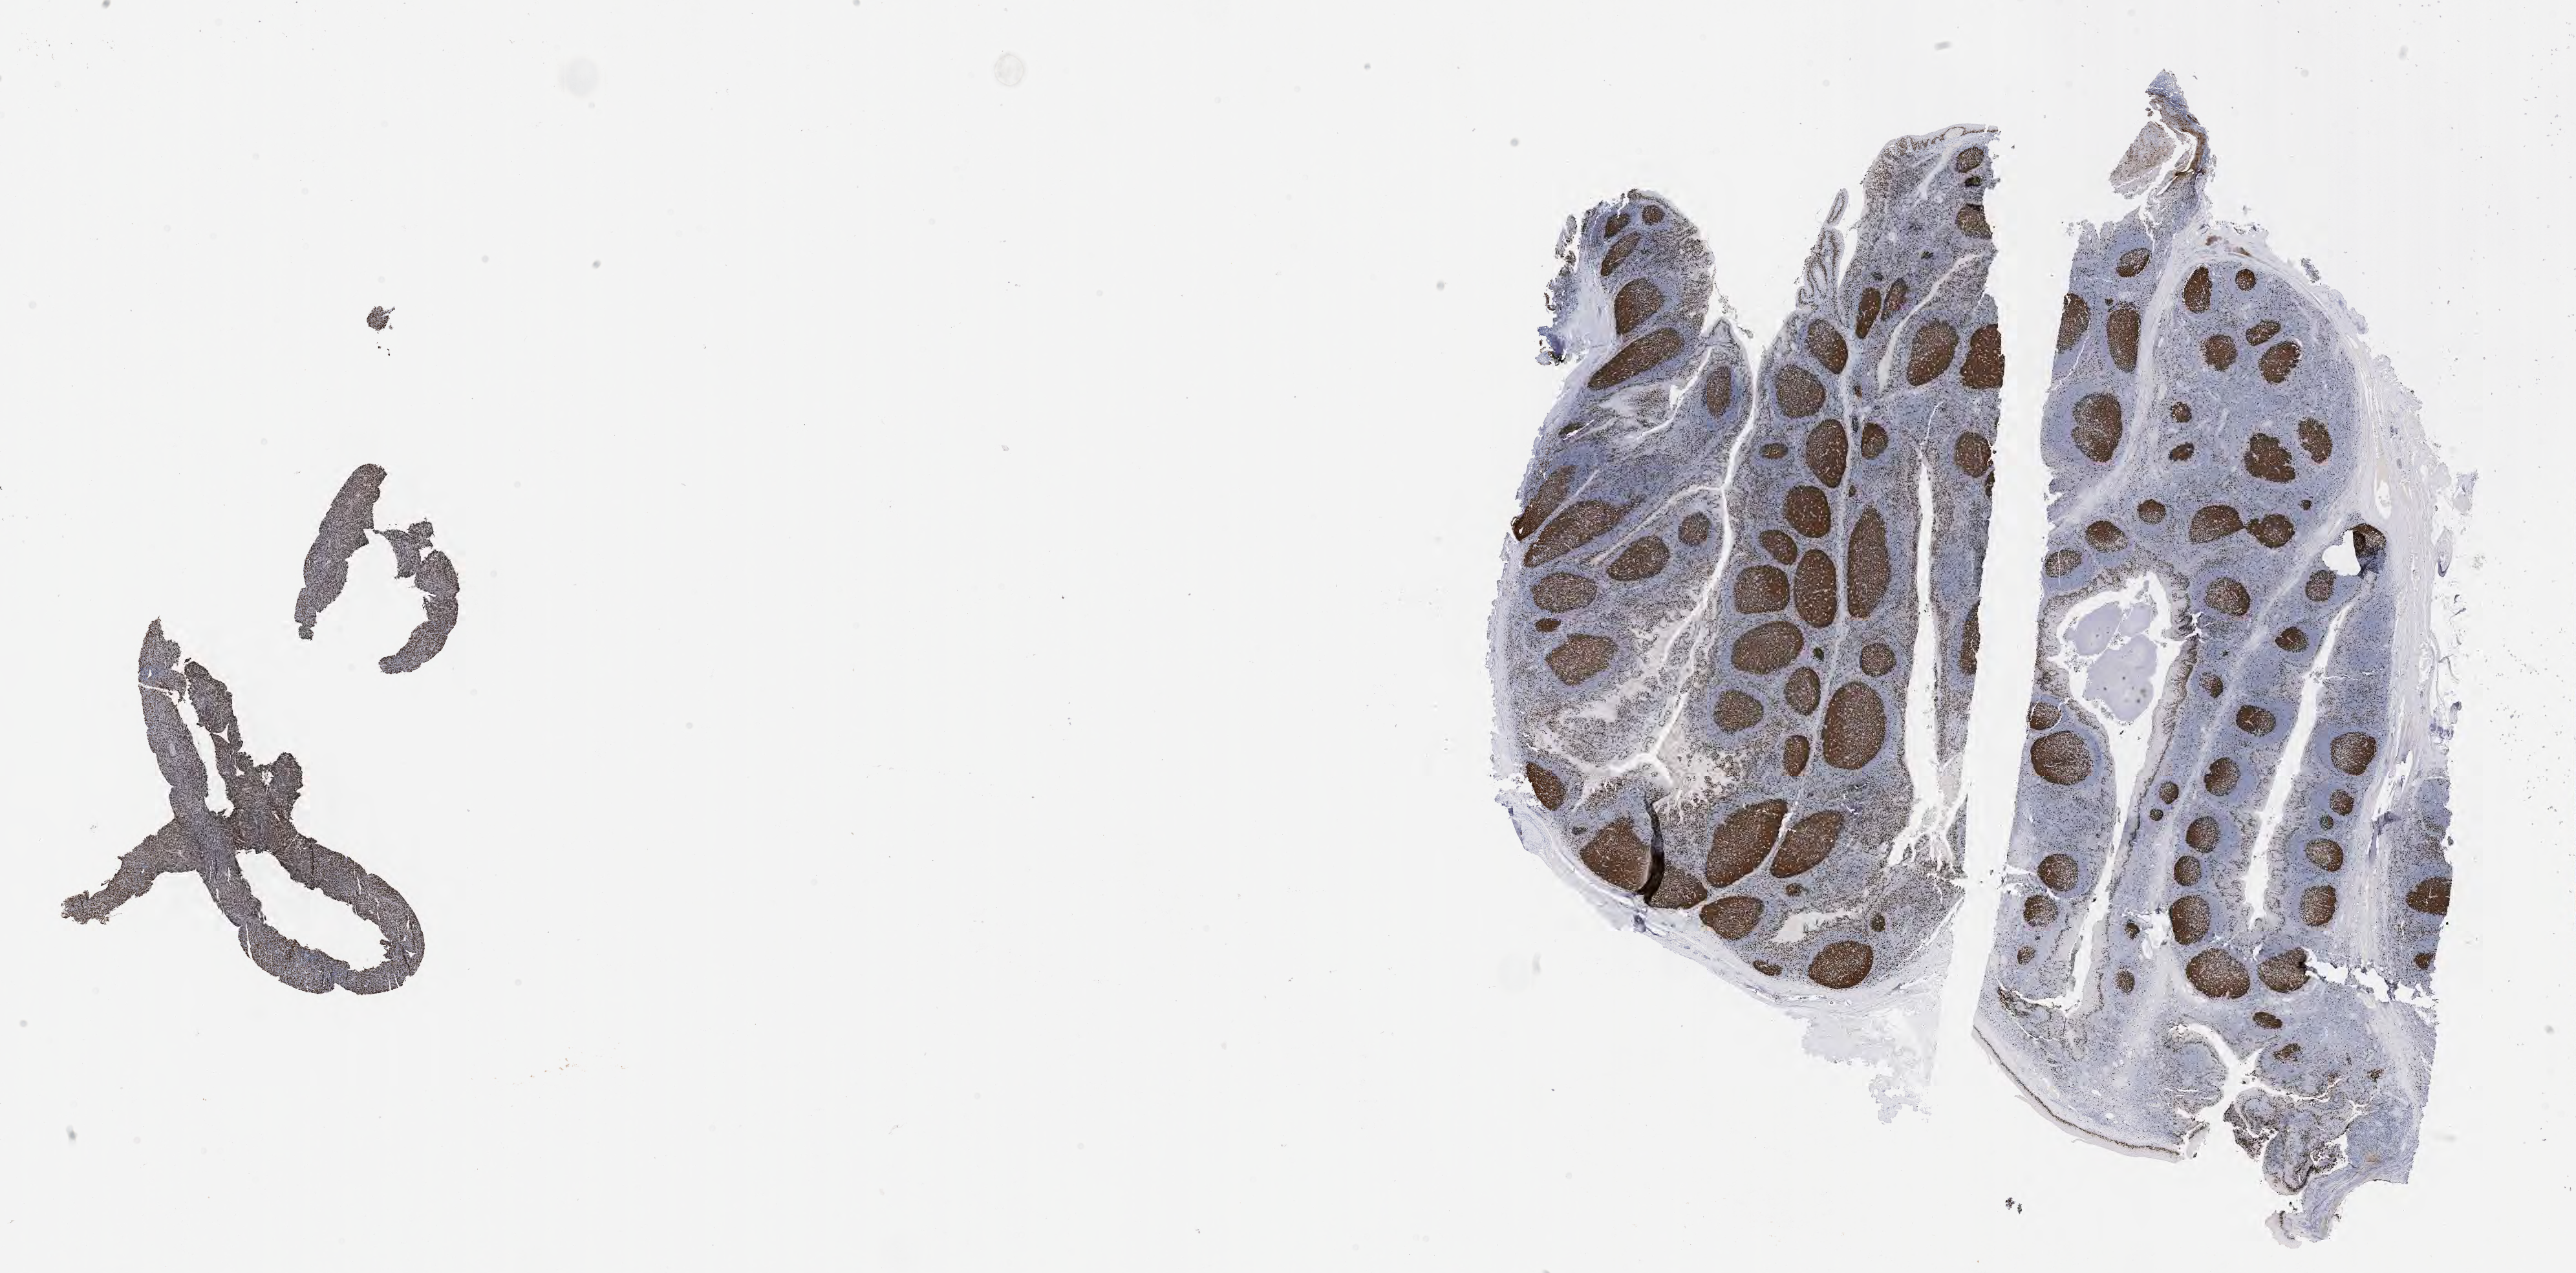
IHC for Ki-67, whole-slide image, low-resolution overview of the scanned area, about 32.2 x 15.9 mm. Patient male; age 52 years.
Specimen: tumor tissue; anatomic site: liver.